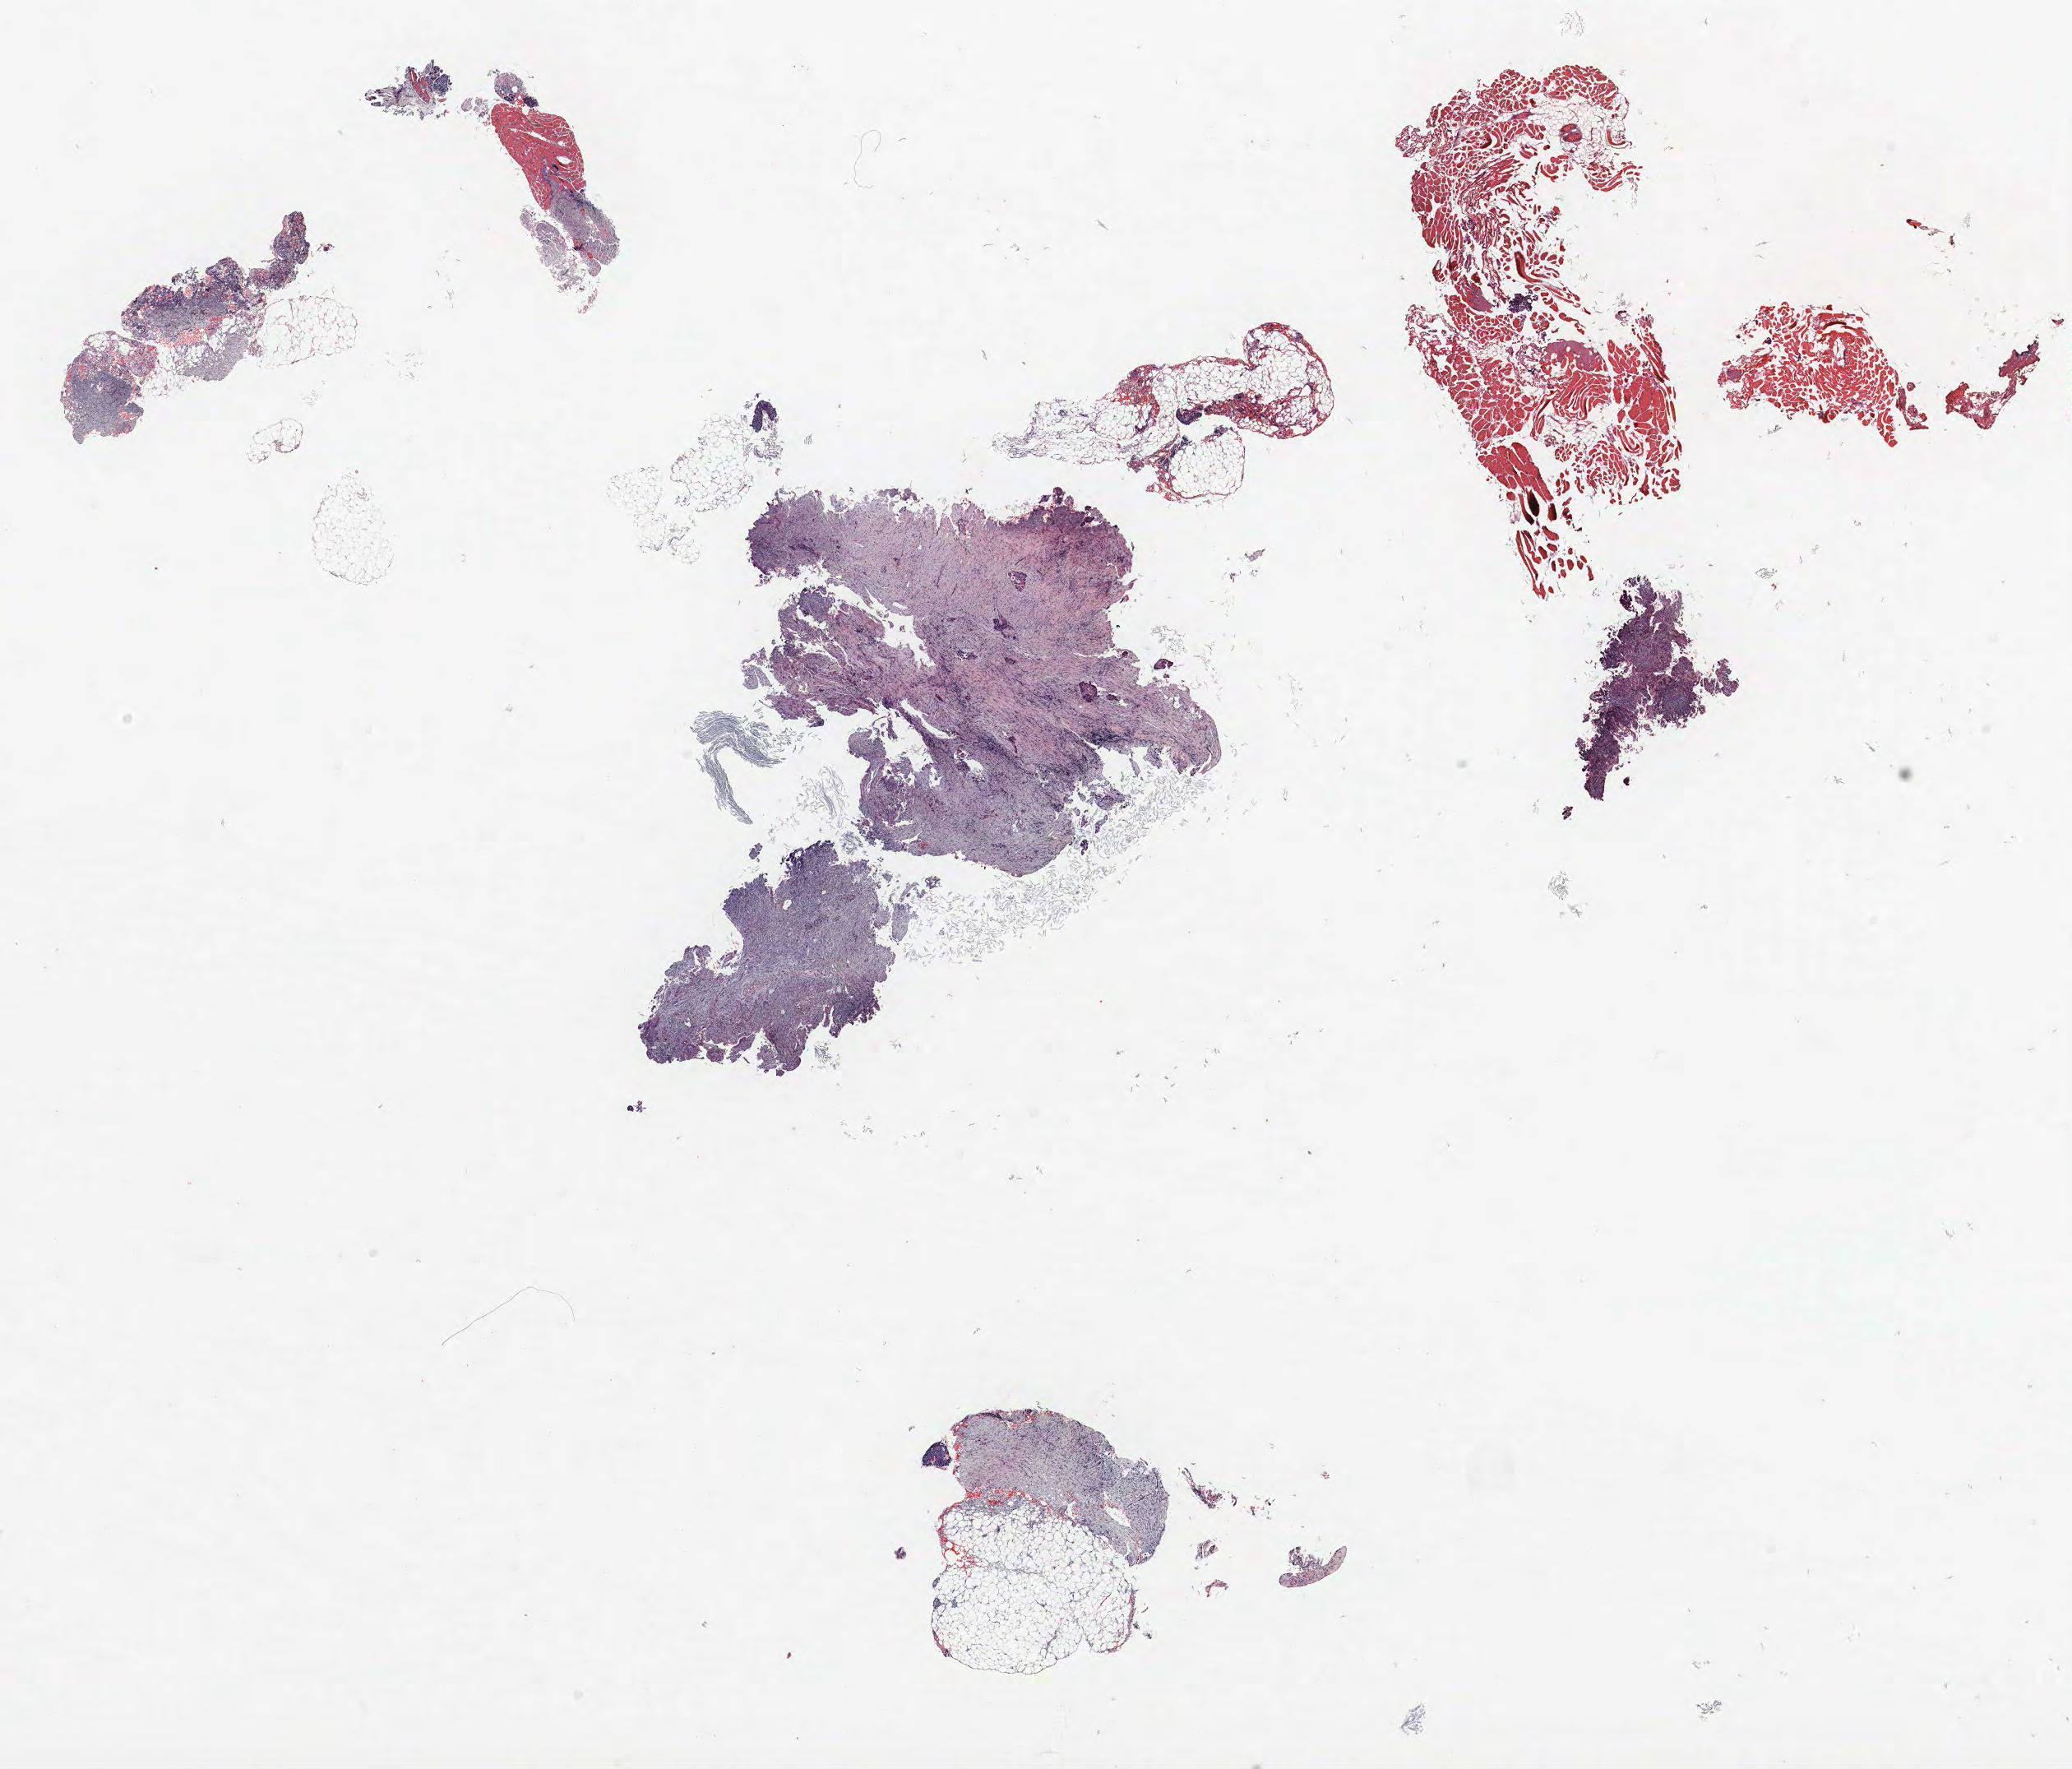
Whole-slide histology image, H&E-stained, shown as a low-resolution overview of the whole scanned area (about 20.2 x 17.2 mm, from a 40x scan). FFPE section. Lung. Male, age 61 at enrolment. Grade: moderately differentiated (G2).
Primary tumour location (clinical record): right middle lobe. Participant's lung-cancer diagnosis: Squamous cell carcinoma, NOS. Tumour size (pathology): 25 mm. ICD-O-3 topography: middle lobe of lung (C34.2). Stage (AJCC 6th edition): IIIB.